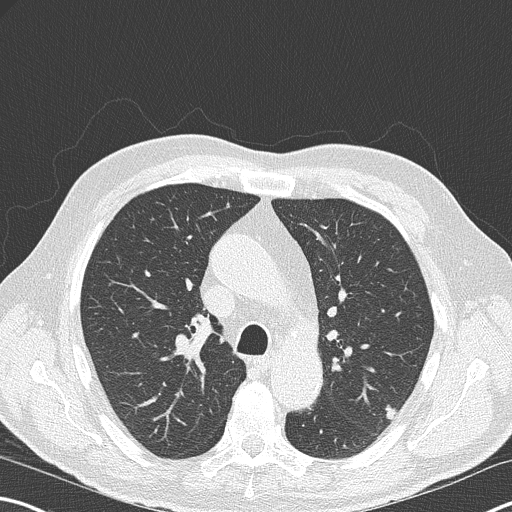
Chest CT (low-dose screening protocol), one axial image, second screening round (one year after baseline), lung window (W 1500 / L -600 HU), lung (sharp) reconstruction kernel (B50f), 120 kVp, slice 73 of 178 in the series, 512 × 512 image matrix. Male, age 67 years at enrolment. Former smoker at enrolment.
Expert reader's lesion annotation, box from (x=369, y=395) to (x=409, y=428) px. Screening reader's record for this exam (one nodule recorded; not confirmed to be the boxed lesion): non-calcified nodule or mass ≥4 mm, left upper lobe, 9 × 6 mm, poorly defined margins, soft tissue attenuation, pre-existing on the prior screen: no. Later outcome: lung cancer diagnosed 418 days after this screen (after the third annual screen) — squamous cell carcinoma, large cell, nonkeratinizing, NOS, left upper lobe, moderately differentiated (G2), stage IA (AJCC 6th edition), 15 mm at pathology.